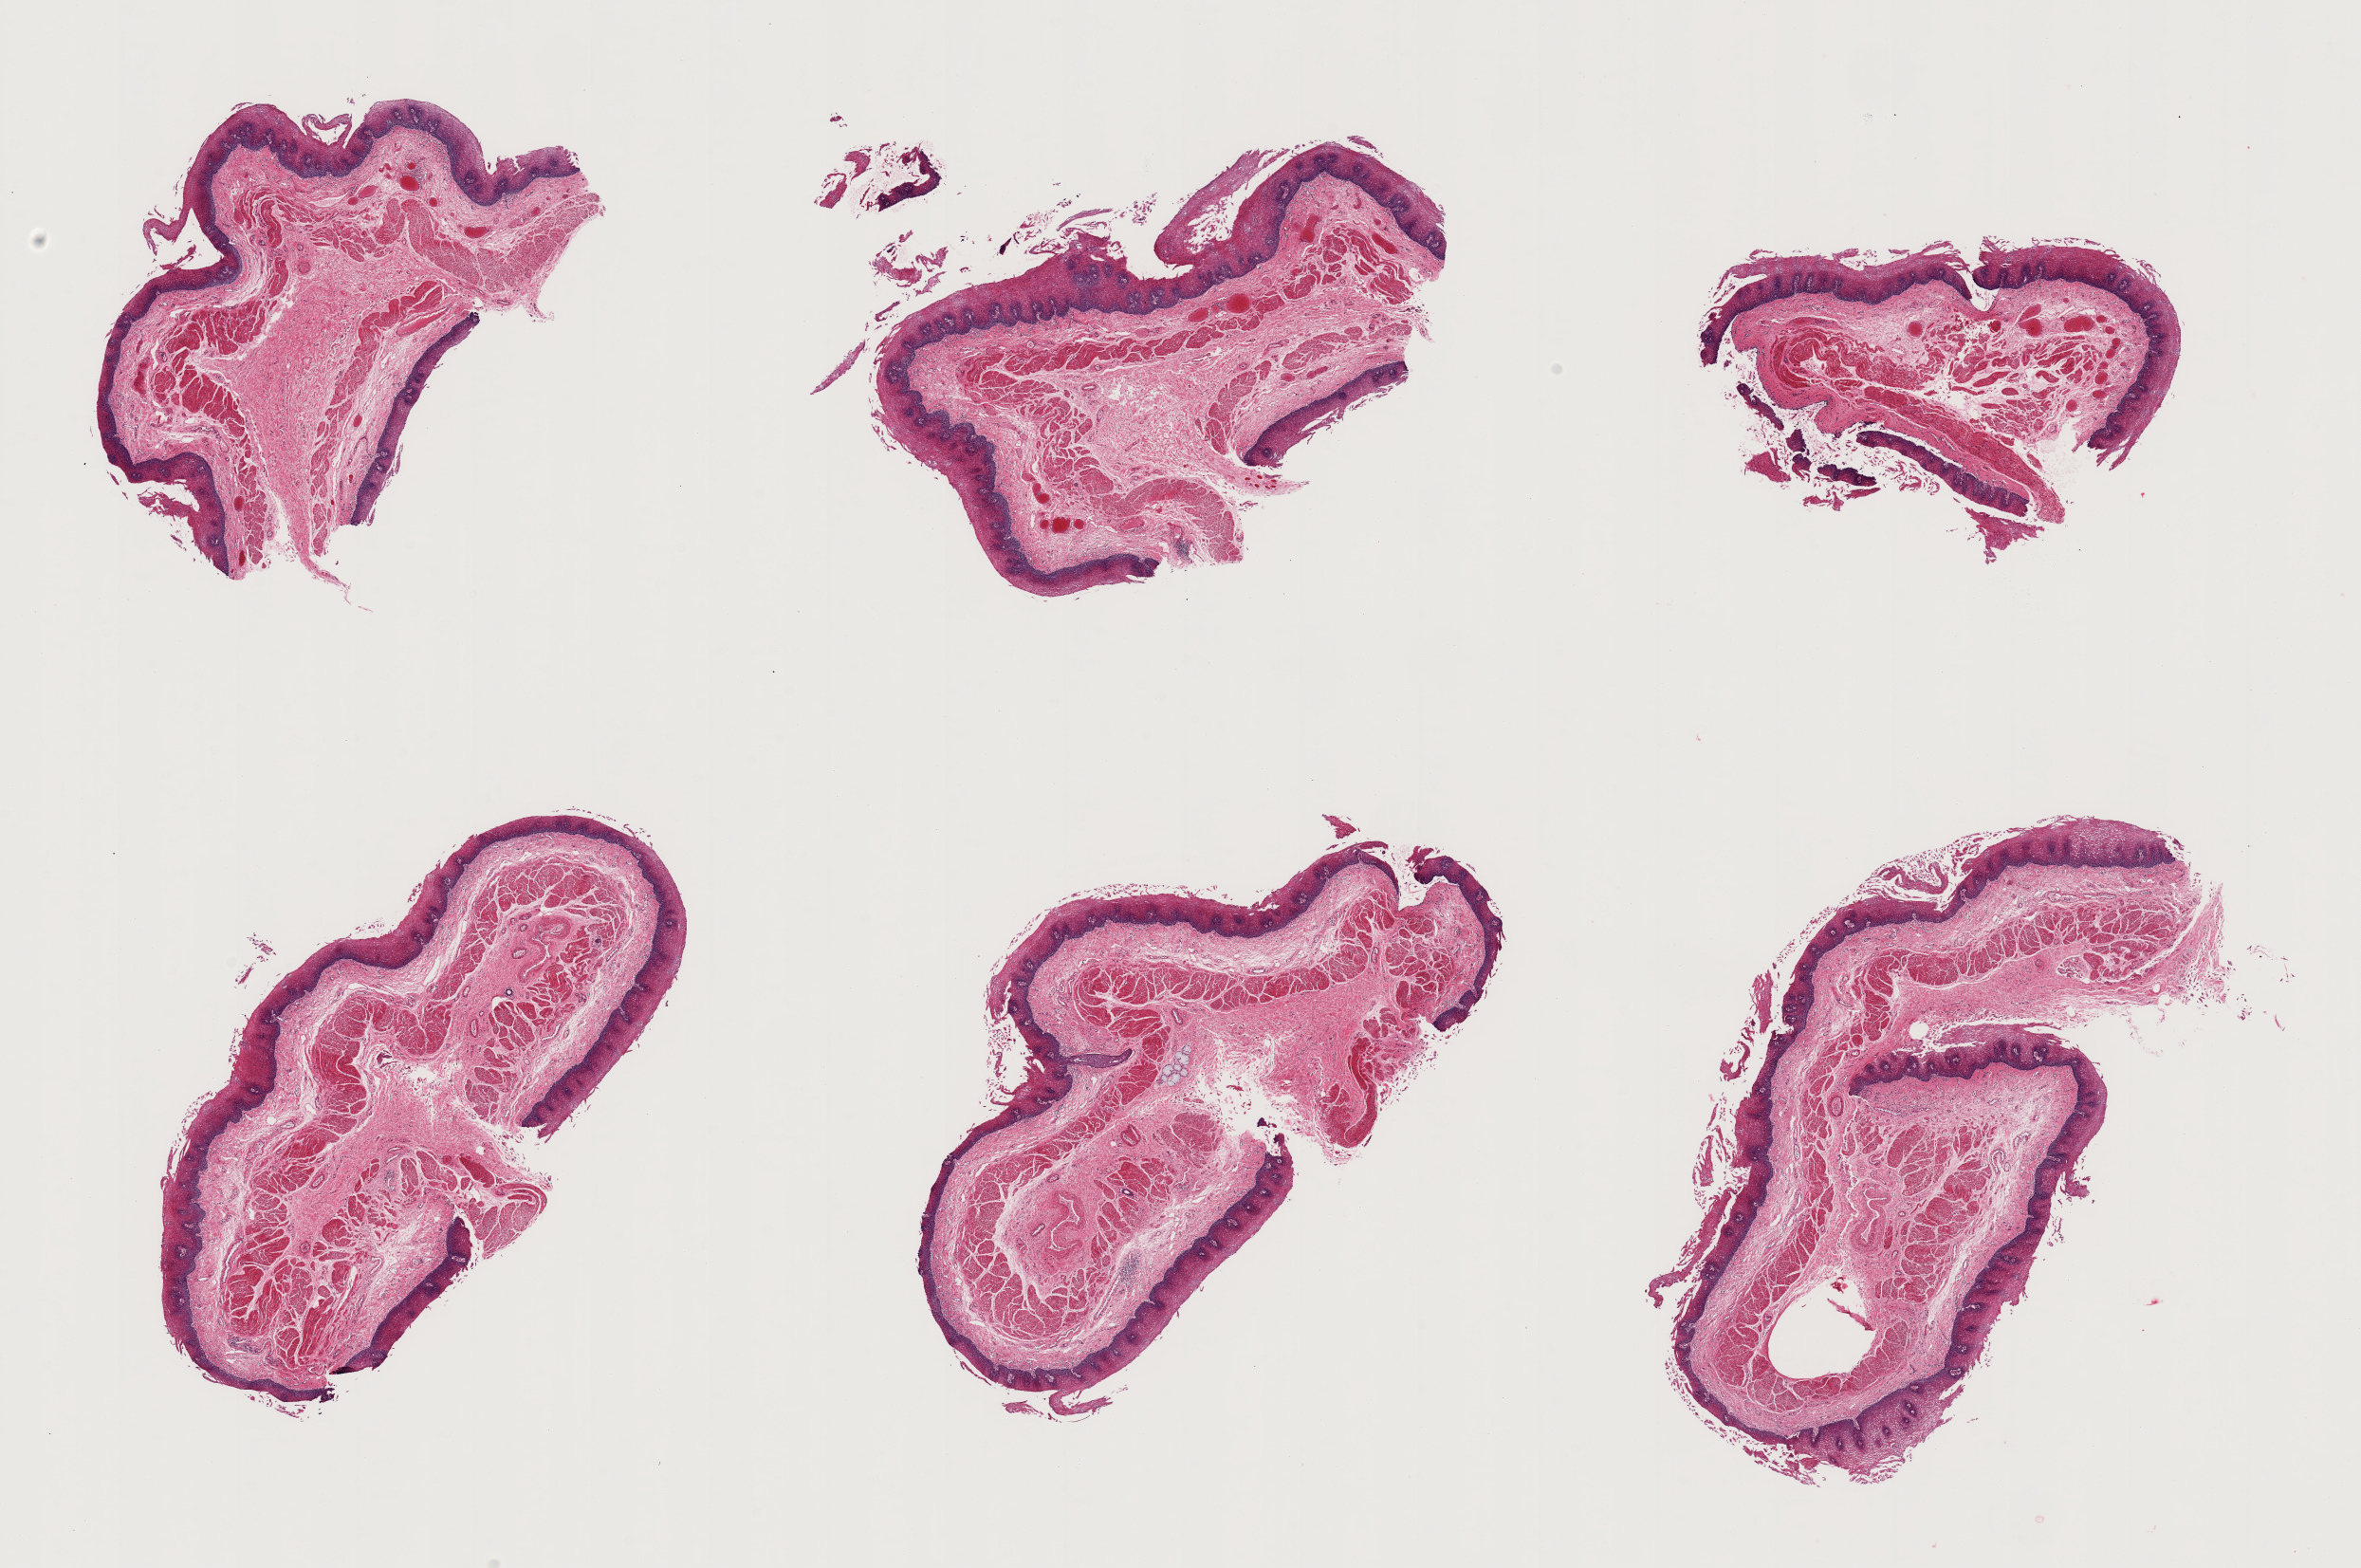
Whole-slide image, haematoxylin and eosin stain — whole scanned area (about 19.7 x 13.1 mm, acquisition: 20x scan) shown as a low-resolution overview, PAXgene-fixed, paraffin-embedded tissue, target tissue: esophageal mucous membrane, tissue donor sample. Donor sex: female.
* pathologist's review note for this sample: 6 pieces; partly fragmented epithelium